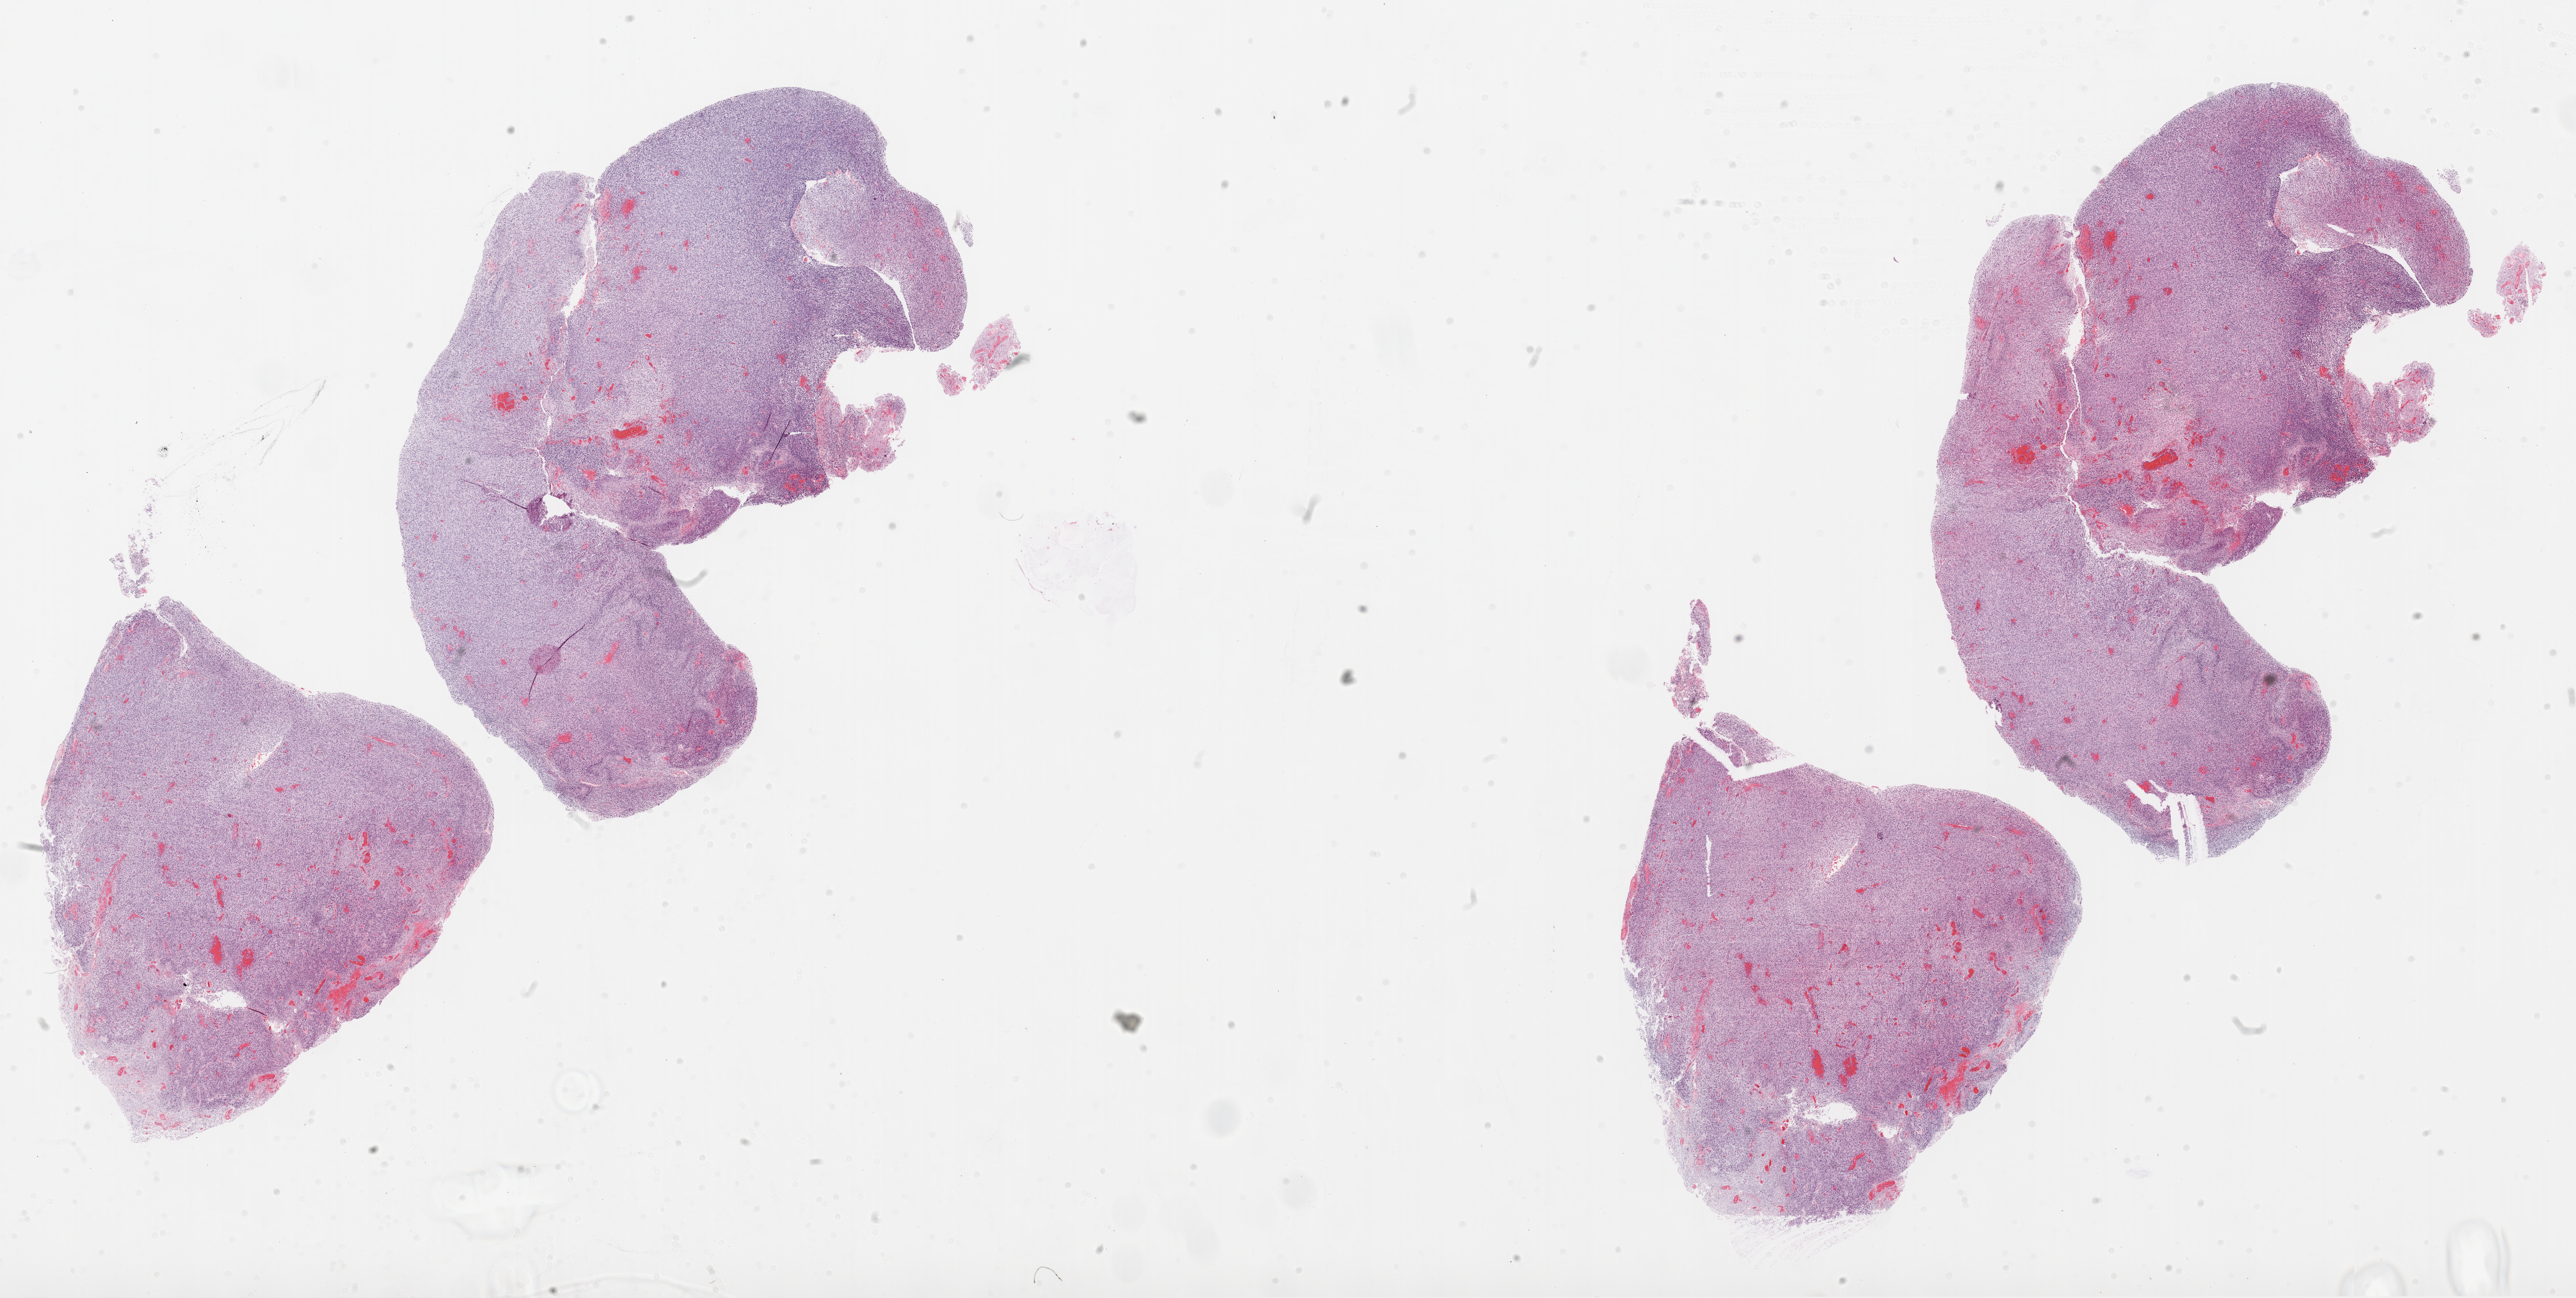
H&E-stained whole-slide image — shown as a low-resolution overview of the whole scanned area (about 35.1 x 17.7 mm, slide scanned at 20x); formalin-fixed paraffin-embedded (FFPE) diagnostic section; brain, primary tumour sample. Male, age 52 years at initial diagnosis.
Histologic diagnosis: Glioblastoma.